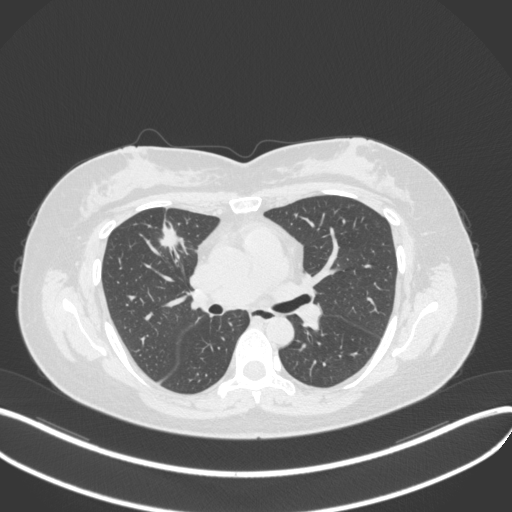
Chest CT, one axial slice; slice 185 of 272 in the series (ordered by position); reconstruction kernel B31f; lung window (W 1500 / L -600 HU); 1 mm slice thickness; 512 × 512 image matrix. Female patient, age 42 years. From the clinical record (not read from this slice): clinical TNM (as recorded): T1b N0 M0.
Outlined on this slice (rectangle marked by the reading radiologist):
- lung tumour (recorded histology: adenocarcinoma): box from (x=152, y=213) to (x=190, y=259) px